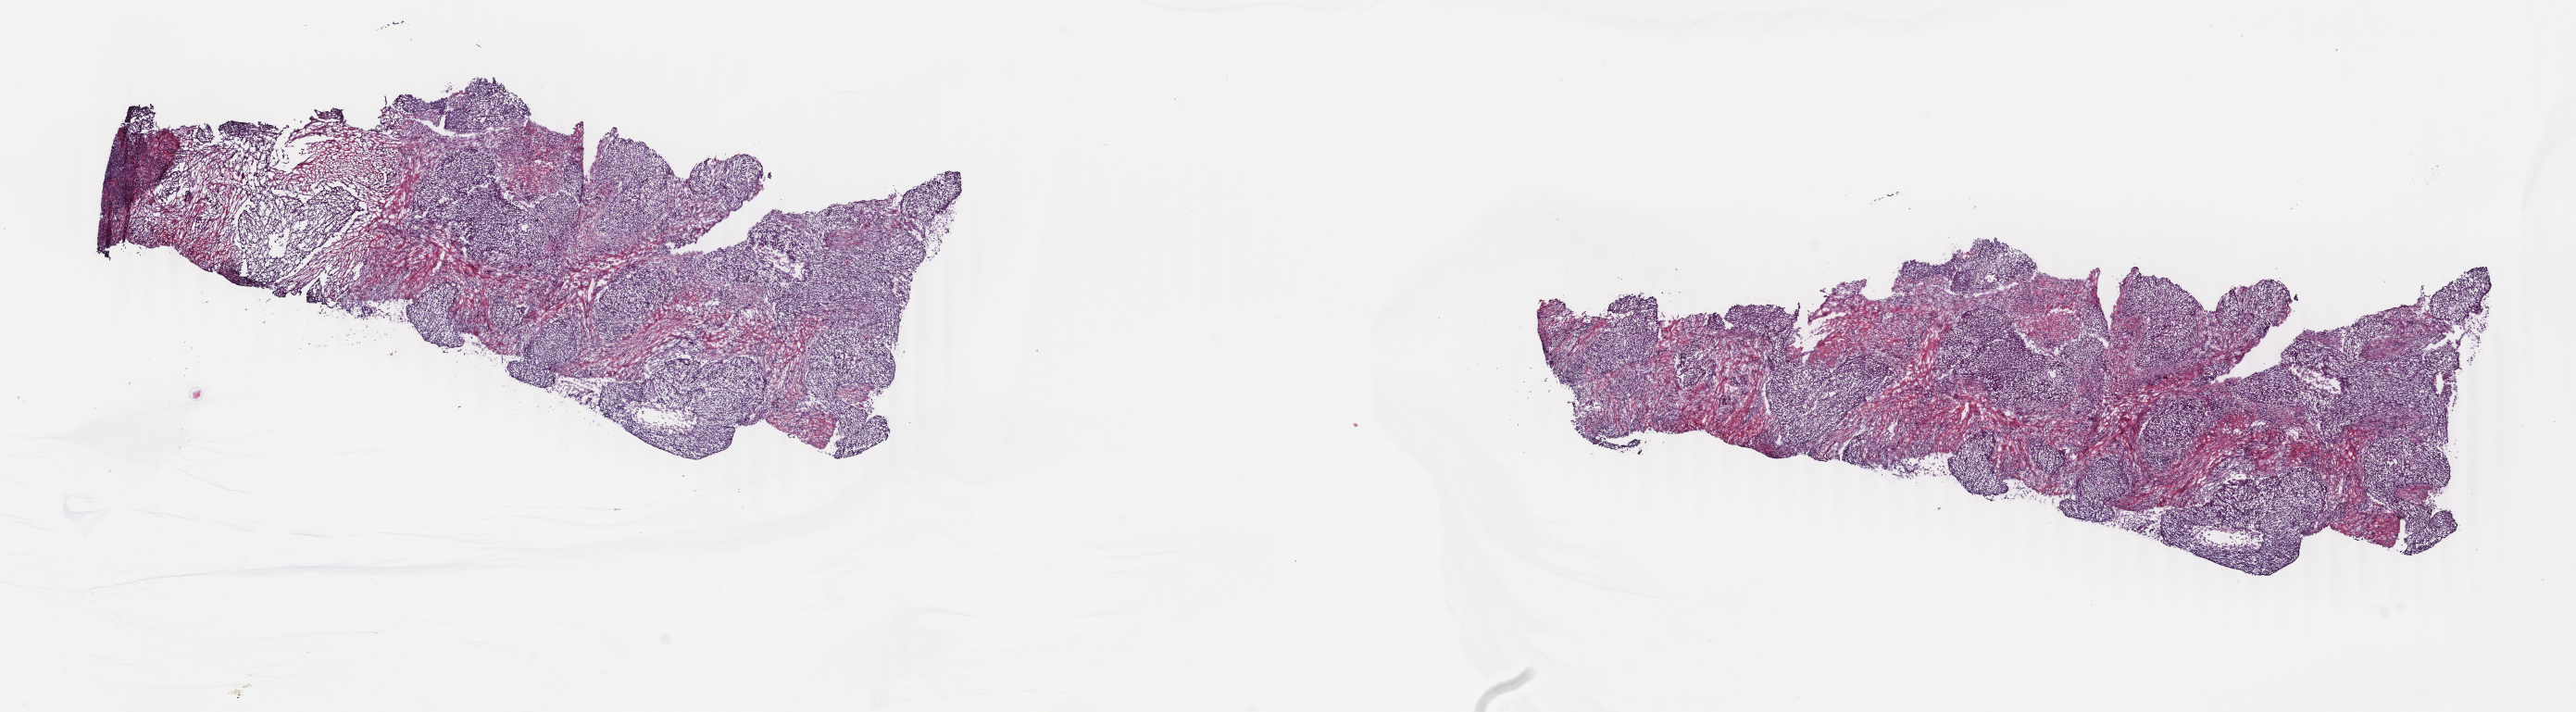
Whole-slide histology image, H&E — a low-resolution overview of the entire scanned area, about 22.1 x 6.1 mm (from a 40x scan); frozen section; sample: primary tumour, cervix. Female, age 51 years at initial diagnosis. Histologic grade: G3 (poorly differentiated). Composition of this section per pathologist review: tumour cells 100%, tumour nuclei 75%, normal cells 0%, stromal cells 0%, necrosis 0%. Infiltration values recorded for this section: lymphocyte infiltration 3%, monocyte infiltration 0%, neutrophil infiltration 0%.
Pathologic diagnosis: Squamous cell carcinoma, NOS (cervix uteri). FIGO stage: IIIB.